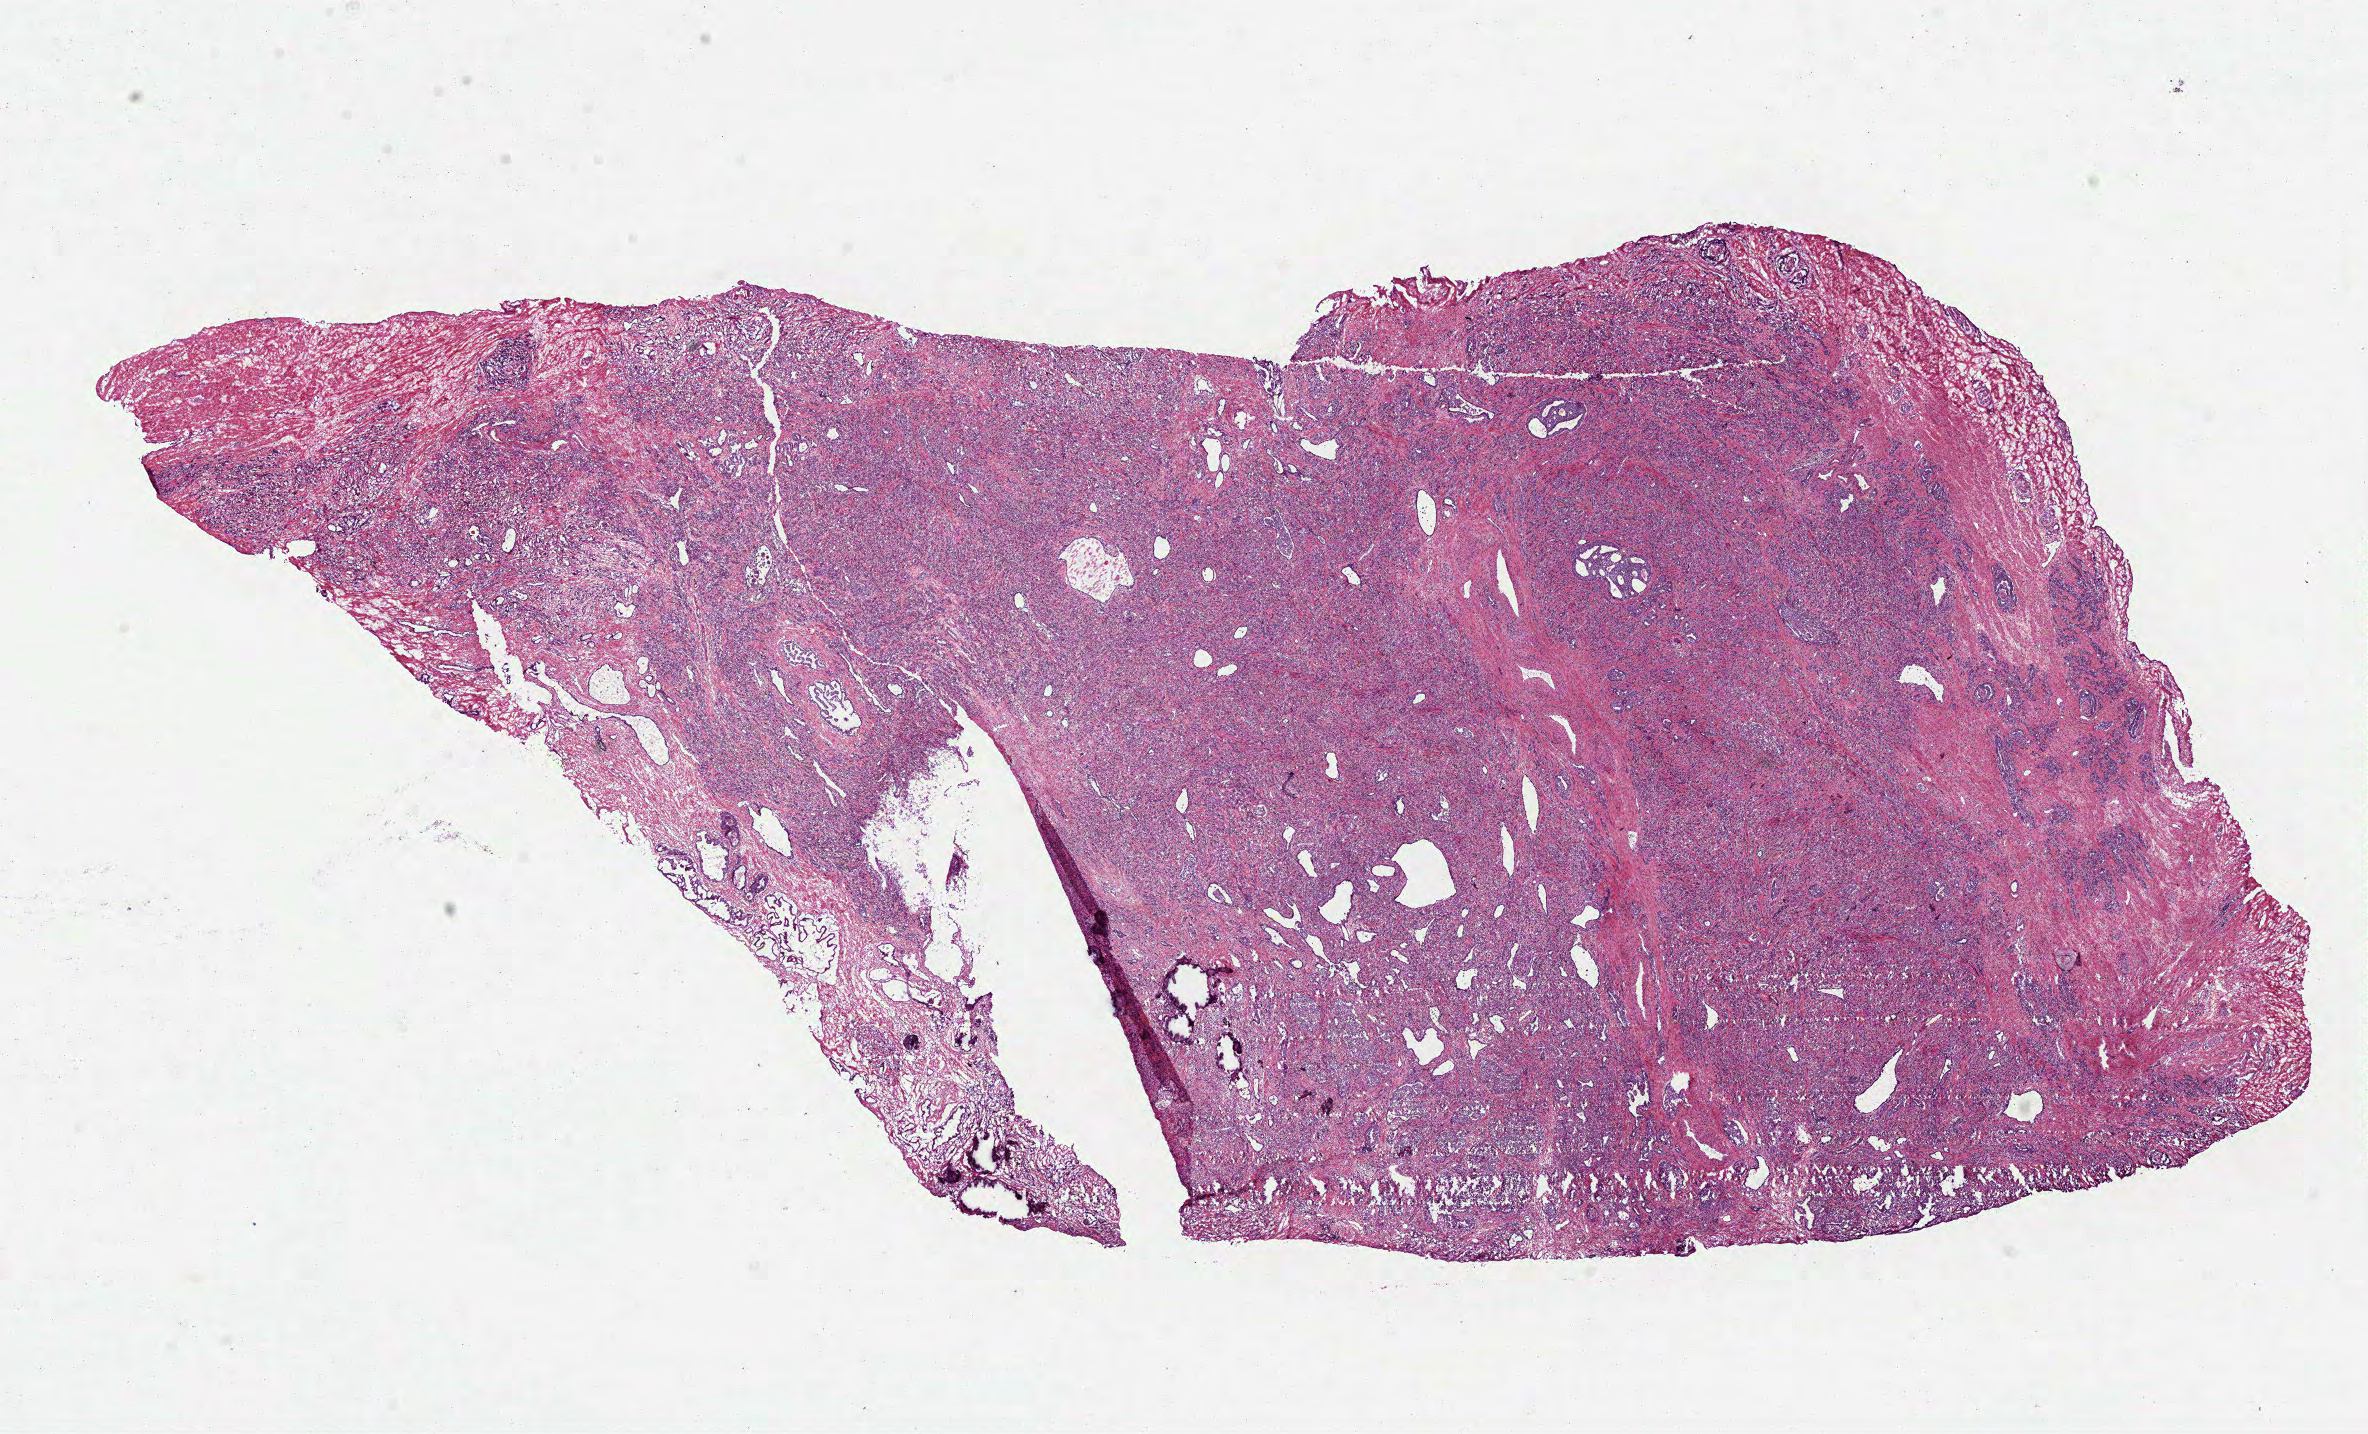
Whole-slide histology image, Hematoxylin and eosin (H&E) stained, low-resolution overview of the scanned area, about 19.1 x 11.6 mm (from a 40x scan), frozen section from the top of the tissue portion, sample: primary tumour, prostate. Male patient; age at initial diagnosis 62 years. Gleason score: 9 (4+5). Composition of this section per pathologist review: tumour cells 87%, tumour nuclei 85%, normal cells 3%, stromal cells 10%, necrosis 0%.
Diagnosis: Acinar cell carcinoma (prostate gland). Lymph nodes positive (case pathology): 0 of 3 examined.